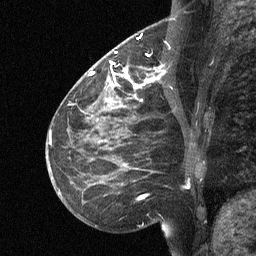
Breast MRI (dynamic contrast-enhanced), one sagittal slice; slice 23 of 64 in the series (ordered by position); dynamic contrast-enhanced study with each time point stored as its own series, time point 2 of 3 at this slice position (early post-contrast, ordered by acquisition time); 1.5 T; TE 4.8 ms, TR 27 ms; 2 mm slice thickness; 256 × 256 image matrix, field of view 200 × 200 mm. Female patient, age 51 years. From the clinical record (not read from this slice): setting: breast cancer imaged before/during neoadjuvant chemotherapy; receptor status: HR-positive, HER2-negative.
Annotated regions visible in this slice (semi-automatic segmentation, software-assisted and operator-edited):
- analysis volume of interest (the breast-tissue region the enhancement analysis was run in; not a lesion): box from (x=112, y=46) to (x=169, y=106) px
- tumour enhancement mask (voxels above the 90 % enhancement threshold inside the analysis volume of interest): (x=112, y=62)–(x=166, y=102)